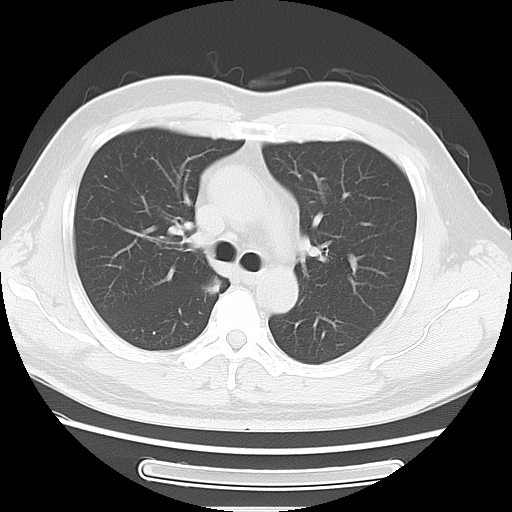
Chest CT, one axial slice. Position 13 of 39 along the scan axis. Reconstruction kernel LUNG. Lung window (W 1500 / L -600 HU). 5 mm slice thickness. 512 × 512 image matrix, field of view 350 × 350 mm. Male patient, age 49 years. From the clinical record (not read from this slice): clinical TNM (as recorded): T1b N0 M0.
Structures marked on this image (rectangle marked by the reading radiologist):
- lung tumour (recorded histology: adenocarcinoma): bounding box (x1, y1, x2, y2) in pixels: (198, 268, 225, 298)